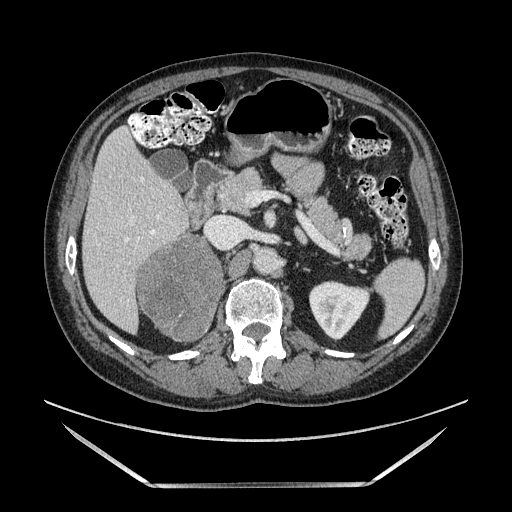
Contrast-enhanced abdominal CT, one axial slice. Position 74 of 185 along the scan axis. Soft-tissue window (W 400 / L 40 HU). 1.25 mm slice thickness. 512 × 512 image matrix, field of view 440 × 440 mm. Male patient. From the clinical record (not read from this slice): diagnosis: adrenocortical carcinoma; tumour side: right adrenal; tumour size at pathology: 10.3 cm; Ki-67 index: 20 %; stage (as recorded): 3.
Outlined on this slice (semi-automatically segmented with operator editing):
- mass: box from (x=140, y=237) to (x=222, y=339) px